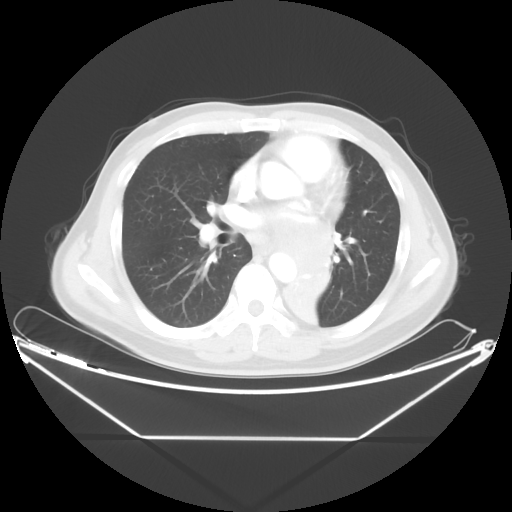
Chest CT, one axial slice; position 23 of 48 along the scan axis; 120 kVp; lung window (W 1500 / L -600 HU); 5 mm slice thickness; 512 × 512 image matrix. Male patient, age 58 years. Case-level facts recorded for this patient, not image findings: clinical TNM (as recorded): T3 N3 M0.
Outlined on this slice (bounding box drawn by a radiologist):
- lung tumour (recorded histology: squamous cell carcinoma): bounding box <281,251,334,318> (left, top, right, bottom; pixels)